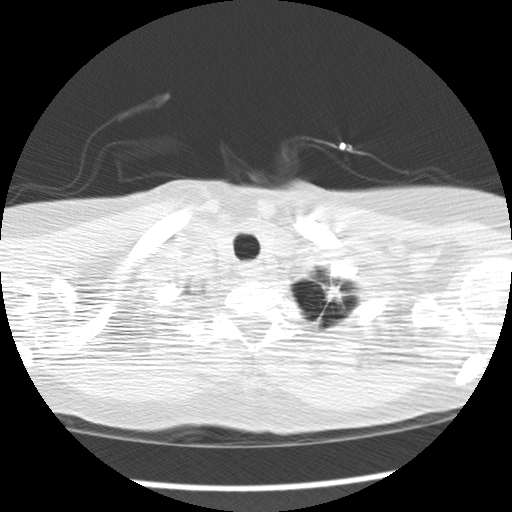
Low-dose screening chest CT, one axial slice; position 152 of 159 along the scan axis; reconstruction kernel STANDARD; 120 kVp; lung window (W 1500 / L -600 HU); 512 × 512 image matrix, field of view 308 × 308 mm.
Annotated regions visible in this slice (manually delineated by an expert):
- lesion 1 (tumor, upper lobe of left lung): bounding box <323,282,347,302> (left, top, right, bottom; pixels)